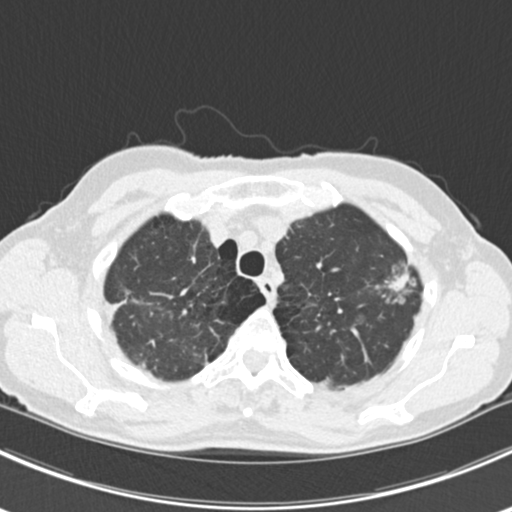
Low-dose screening chest CT, axial slice. First (baseline) screen. Lung window (W 1500 / L -600 HU). 2 mm slice thickness. Standard (soft-tissue) reconstruction kernel (B30f). 120 kVp. Slice 37 of 224 in the series. Female participant, aged 63 years at enrolment. Current smoker at enrolment.
Expert-annotated lung lesion, bounding box (x1, y1, x2, y2) in pixels: (366, 255, 426, 316). The screening reader recorded 10 non-calcified nodules or masses ≥4 mm on this exam (right lower lobe, right lower lobe, left lower lobe, left lower lobe, right middle lobe, right lower lobe, left lower lobe, left upper lobe, right upper lobe, left upper lobe); which of them this box marks is not recorded. Official screen result: positive, change unspecified: nodule(s) >= 4 mm or enlarging nodule(s), mass(es), or other non-specific abnormalities suspicious for lung cancer.